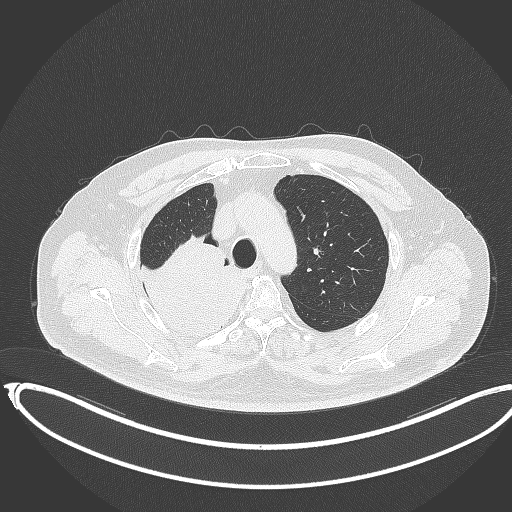
Chest CT, one axial slice; position 282 of 403 along the scan axis; lung window (W 1500 / L -600 HU); 512 × 512 image matrix, field of view 436 × 436 mm. Patient: male, 68 years. Case-level facts recorded for this patient, not image findings: clinical TNM (as recorded): T2a N0 M0.
Structures marked on this image (bounding box drawn by a radiologist):
- lung tumour (recorded histology: adenocarcinoma): bounding box [x1, y1, x2, y2] px = [138, 240, 251, 346]